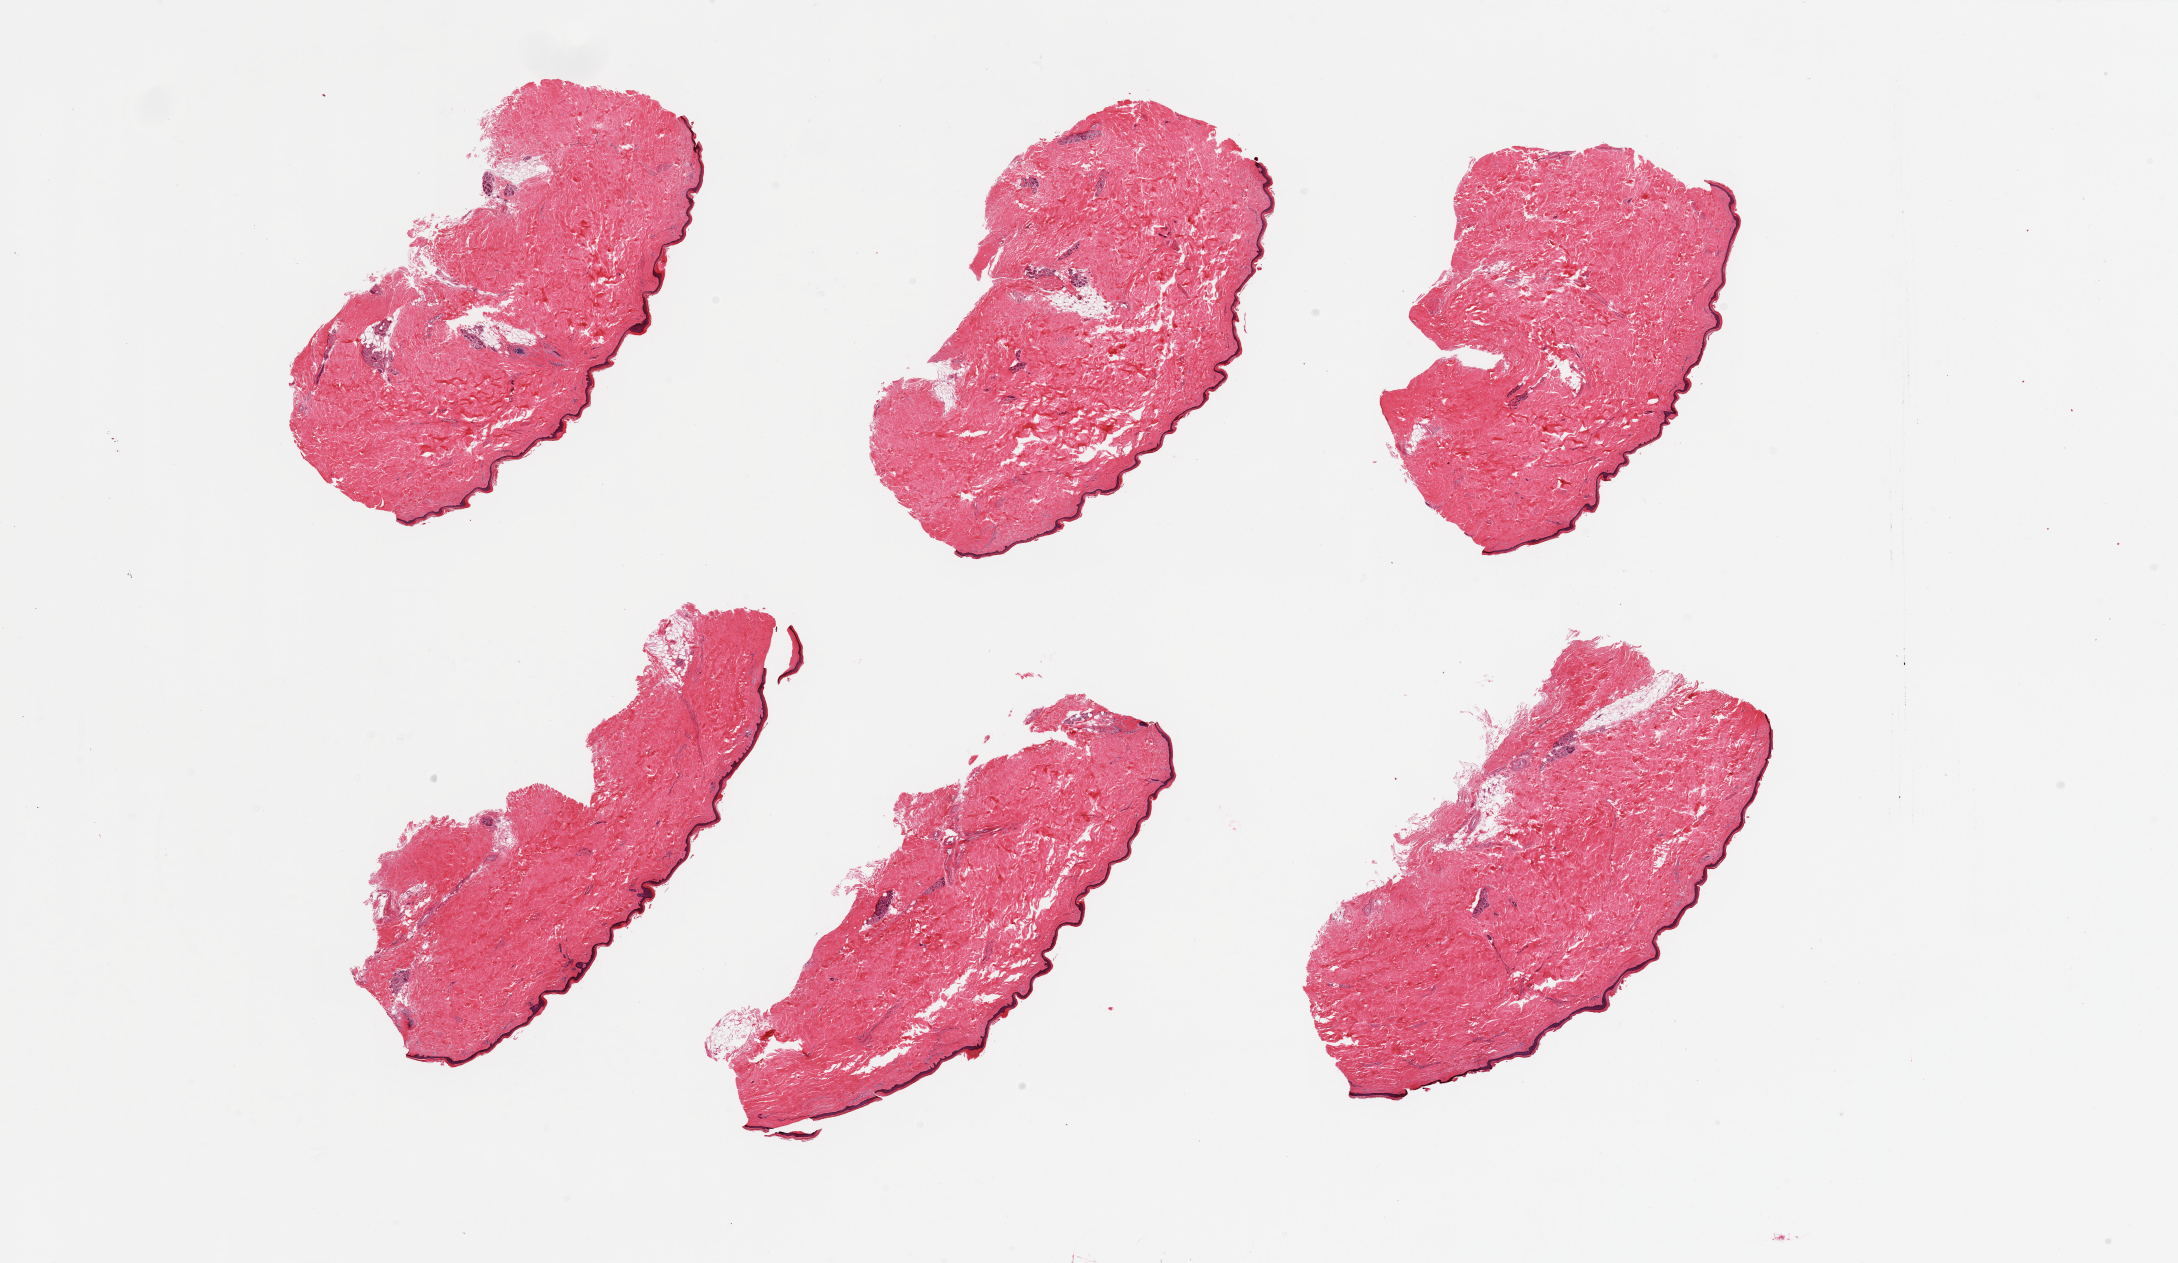
Whole-slide image, hematoxylin and eosin (H&E) stain, whole scanned area (about 34.5 x 20.0 mm) shown as a low-resolution overview, PAXgene-fixed paraffin-embedded (PFPE) section, sampled site (target tissue): skin of lower leg, tissue donor sample. Male donor.
Reviewer comment on this tissue sample: 6 pieces, no dermal fat; squamous epithelium is ~40 microns.